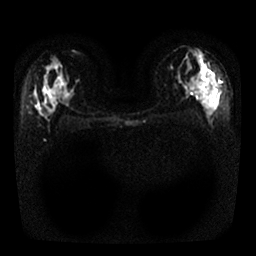
Breast MRI, one axial slice; position 14 of 25 along the scan axis; diffusion-weighted series; image 2 of 4 stored at this slice position (different b-values; order by instance number); 1.5 T; 4 mm slice thickness; 256 × 256 image matrix, field of view 320 × 320 mm. Female patient.
Outlined on this slice (outlined manually by an expert reader):
- tumour on diffusion-weighted imaging: box from (x=205, y=71) to (x=221, y=101) px